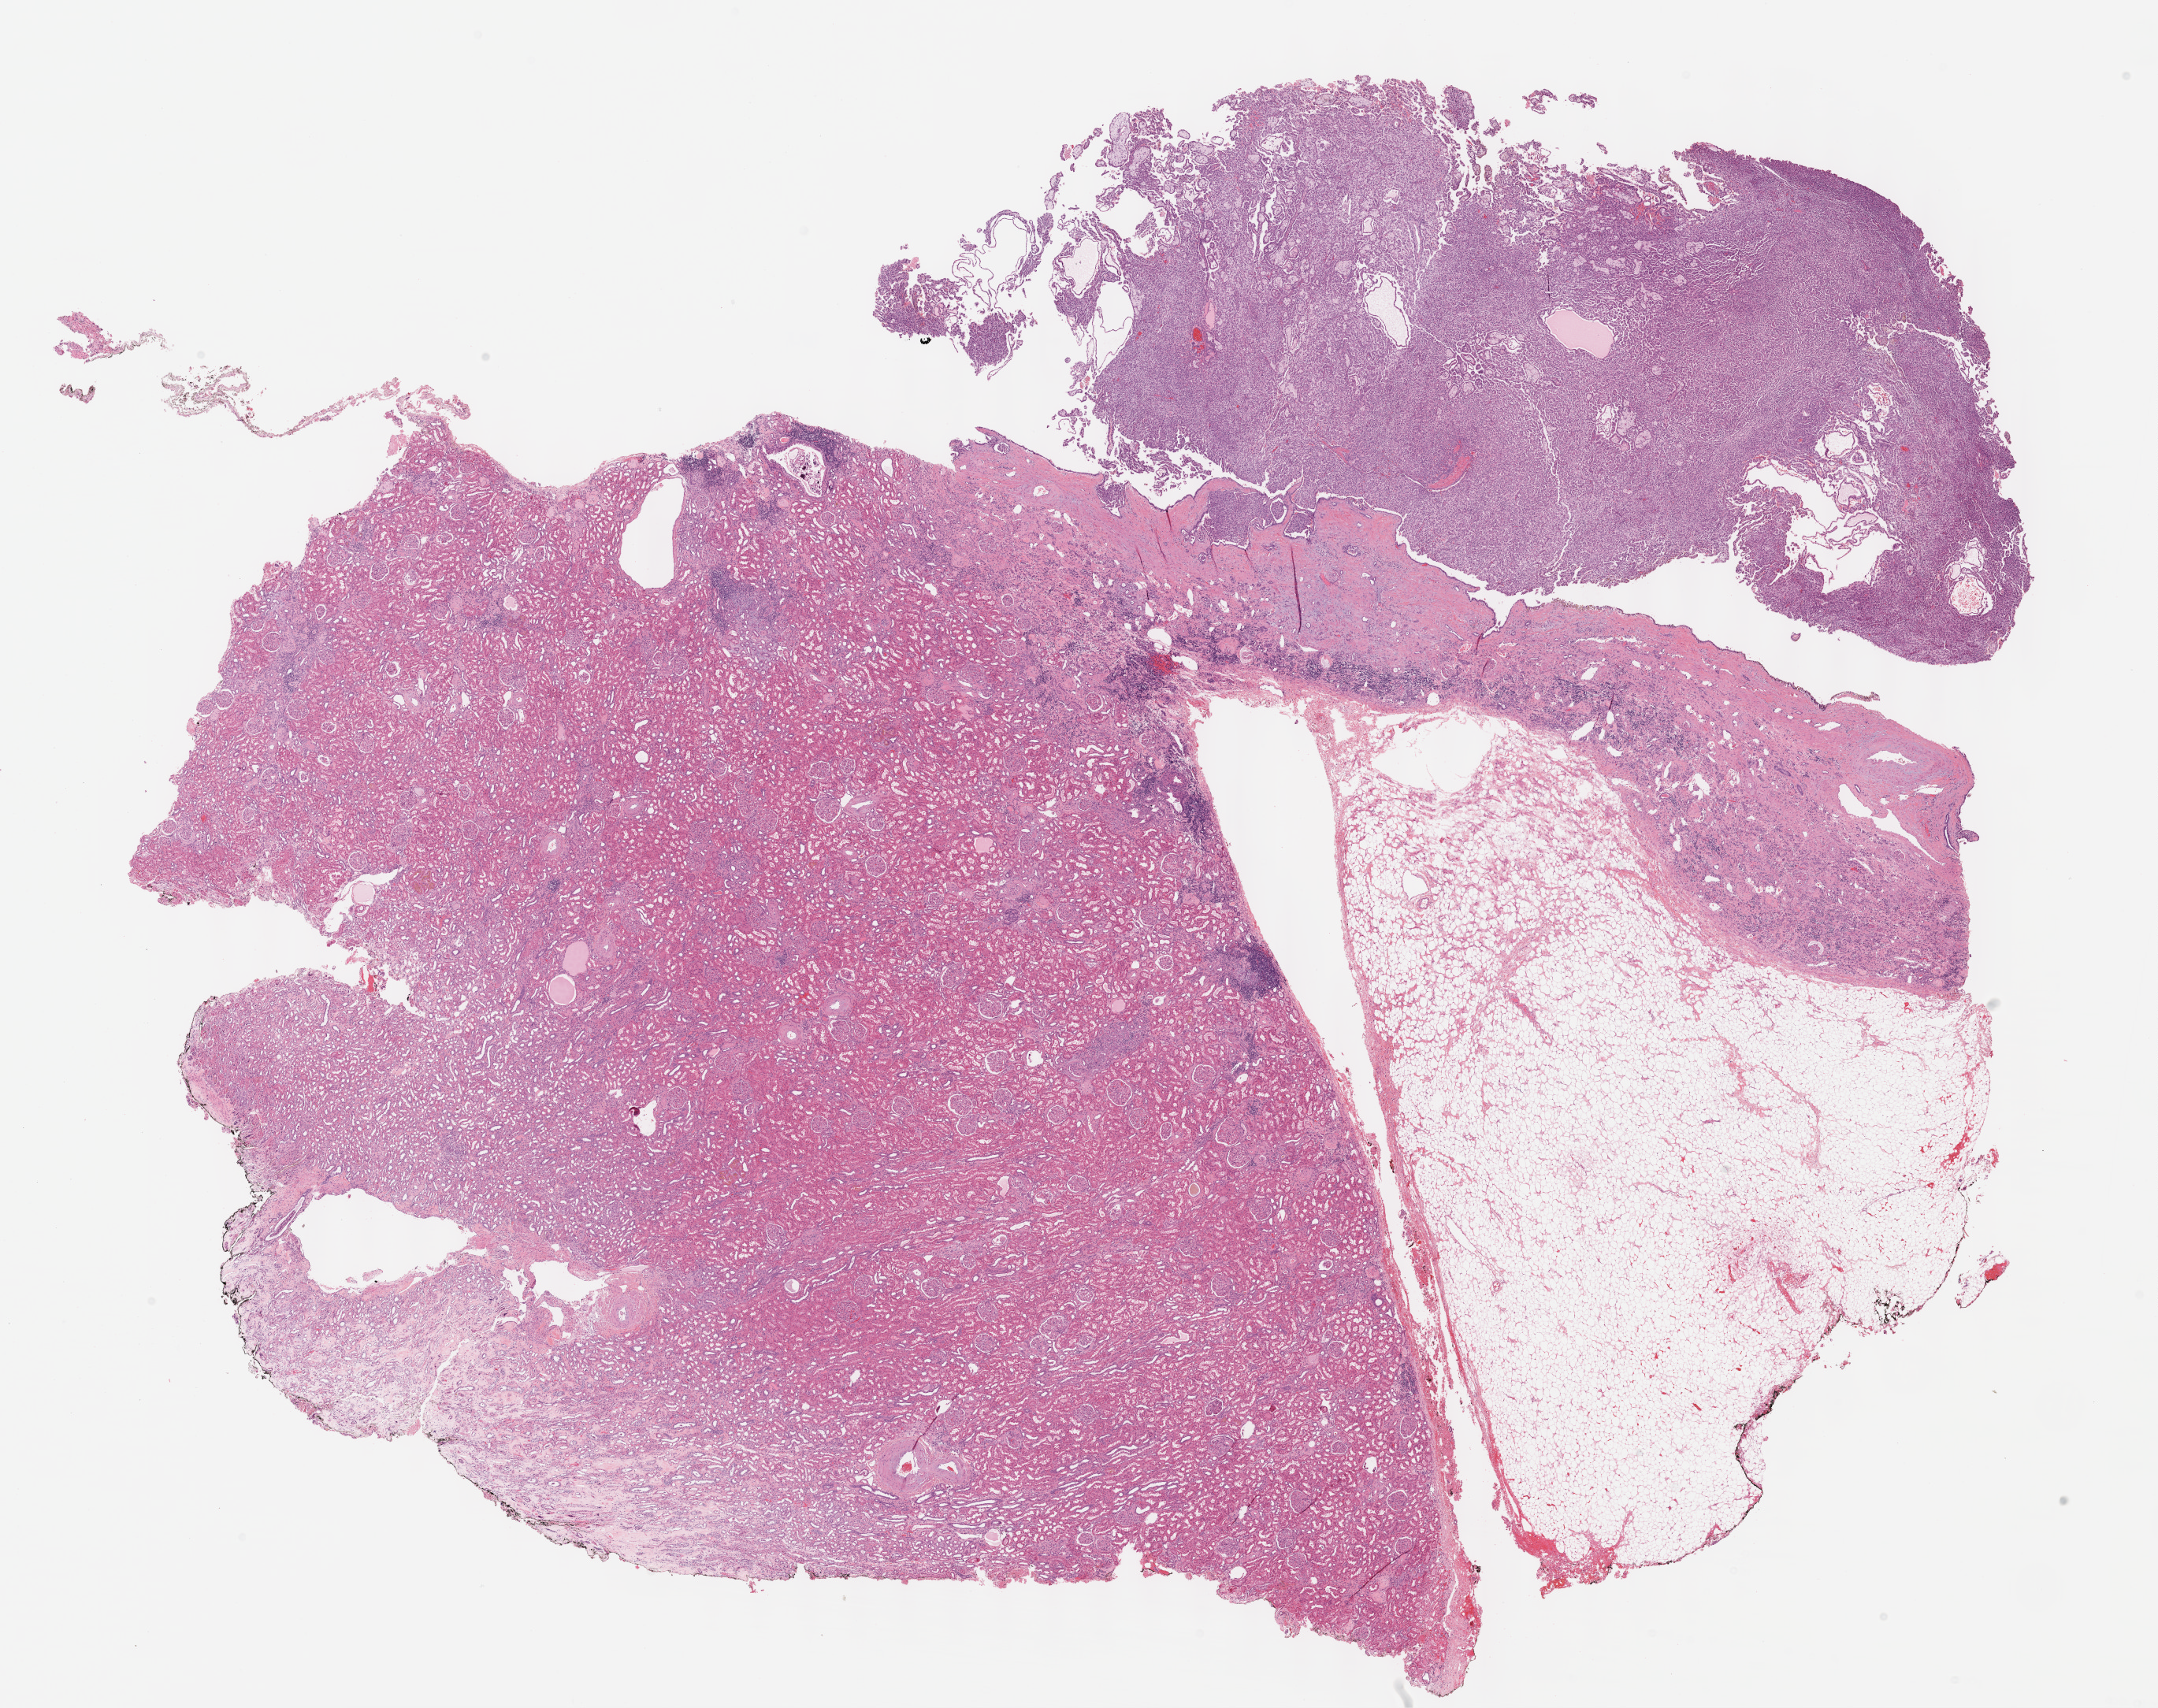
Hematoxylin and eosin (H&E) stained whole-slide image — shown as a low-resolution overview of the whole scanned area (about 22.1 x 17.5 mm, slide scanned at 40x). Formalin-fixed paraffin-embedded (FFPE) diagnostic section. Primary tumour sample from the kidney. Patient: male, age at initial diagnosis 77 years.
* TNM: T1b NX MX
* laterality: right
* AJCC pathologic stage: I (6th edition)
* pathologic diagnosis: Papillary adenocarcinoma, NOS